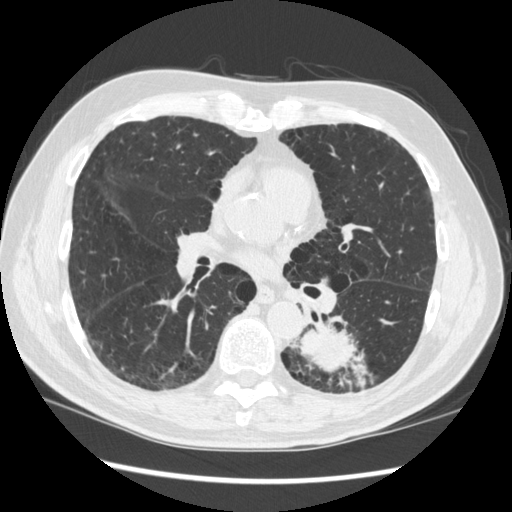
Low-dose screening chest CT, one axial slice; slice 164 of 348 in the series (ordered by position); 120 kVp; lung window (W 1500 / L -600 HU); 1.25 mm slice thickness; 512 × 512 image matrix.
Outlined on this slice (expert manual segmentation):
- lesion 1 (tumor, lower lobe of left lung): box from (x=292, y=327) to (x=373, y=387) px